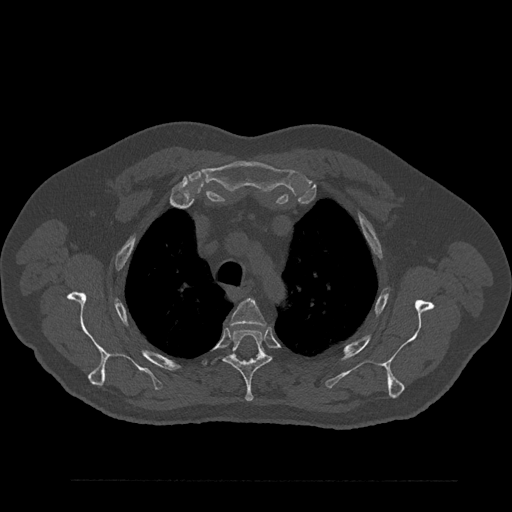
CT including the spine, one axial slice. Slice 650 of 797 in the series (ordered by position). Bone window (W 1800 / L 400 HU). 0.5 mm slice thickness. 512 × 512 image matrix. Patient: male, 61 years. Case-level facts recorded for this patient, not image findings: primary cancer: prostate.
Structures marked on this image (semi-automatic segmentation, software-assisted and operator-edited):
- T3 vertebra: bounding box <230,299,266,326> (left, top, right, bottom; pixels)
- T4 vertebra: <224,329,271,402>